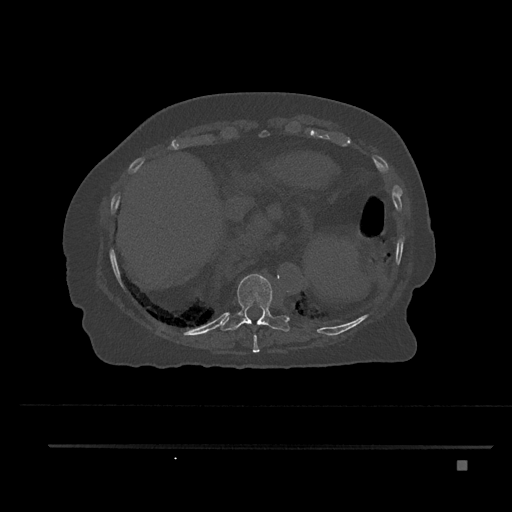
CT including the spine, one axial slice. Slice 363 of 797 in the series (ordered by position). Reconstruction kernel Br40s/3. Bone window (W 1800 / L 400 HU). 0.5 mm slice thickness. 512 × 512 image matrix, field of view 437 × 437 mm. Patient: female, 76 years. From the clinical record (not read from this slice): primary cancer: lung; vertebrae with lytic lesions (as recorded): T11, L3.
Structures marked on this image (semi-automatic segmentation, software-assisted and operator-edited):
- T10 vertebra: bounding box (x1, y1, x2, y2) in pixels: (220, 274, 290, 332)
- T9 vertebra: (253, 334, 260, 353)